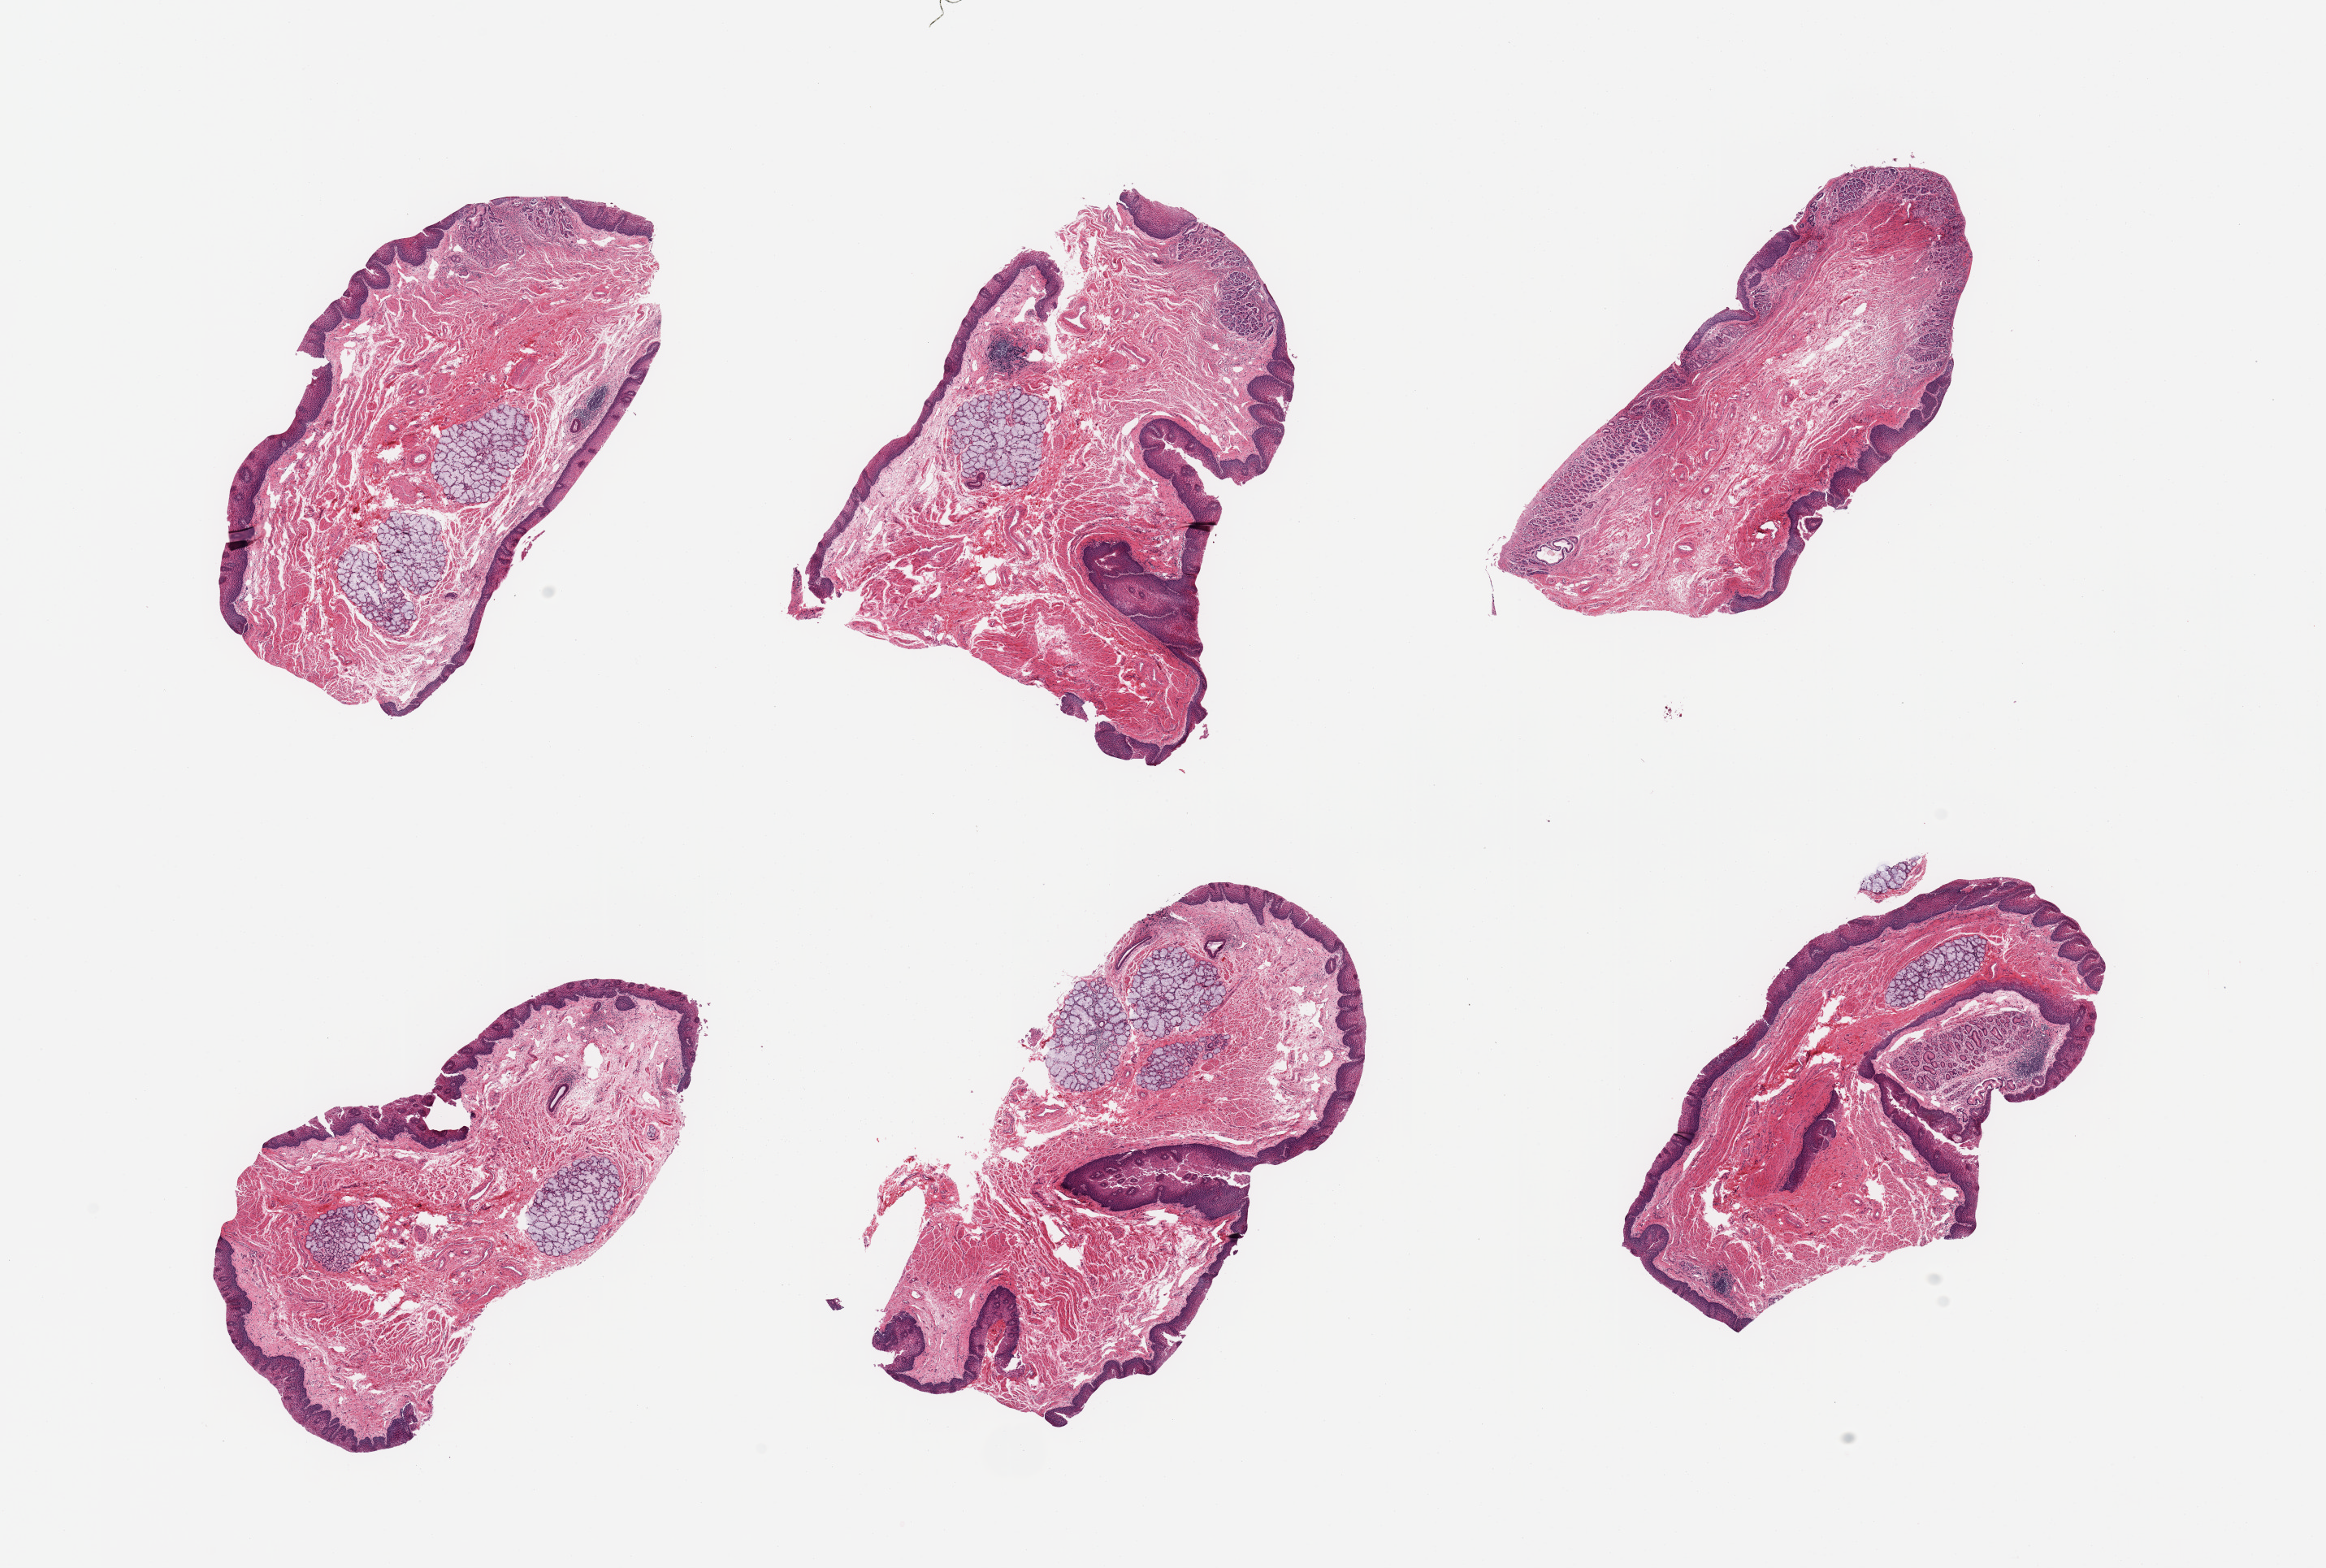
Whole-slide image, H&E stain, brightfield — low-resolution overview of the scanned area, about 22.6 x 15.3 mm; PAXgene-fixed, paraffin-embedded tissue; target tissue: gastroesophageal junction; tissue donor sample. Donor sex: male.
Review note (as recorded): 6 pieces, GEJ mucosa, not correct site, reflux inflammation present; prominent mucus glands.